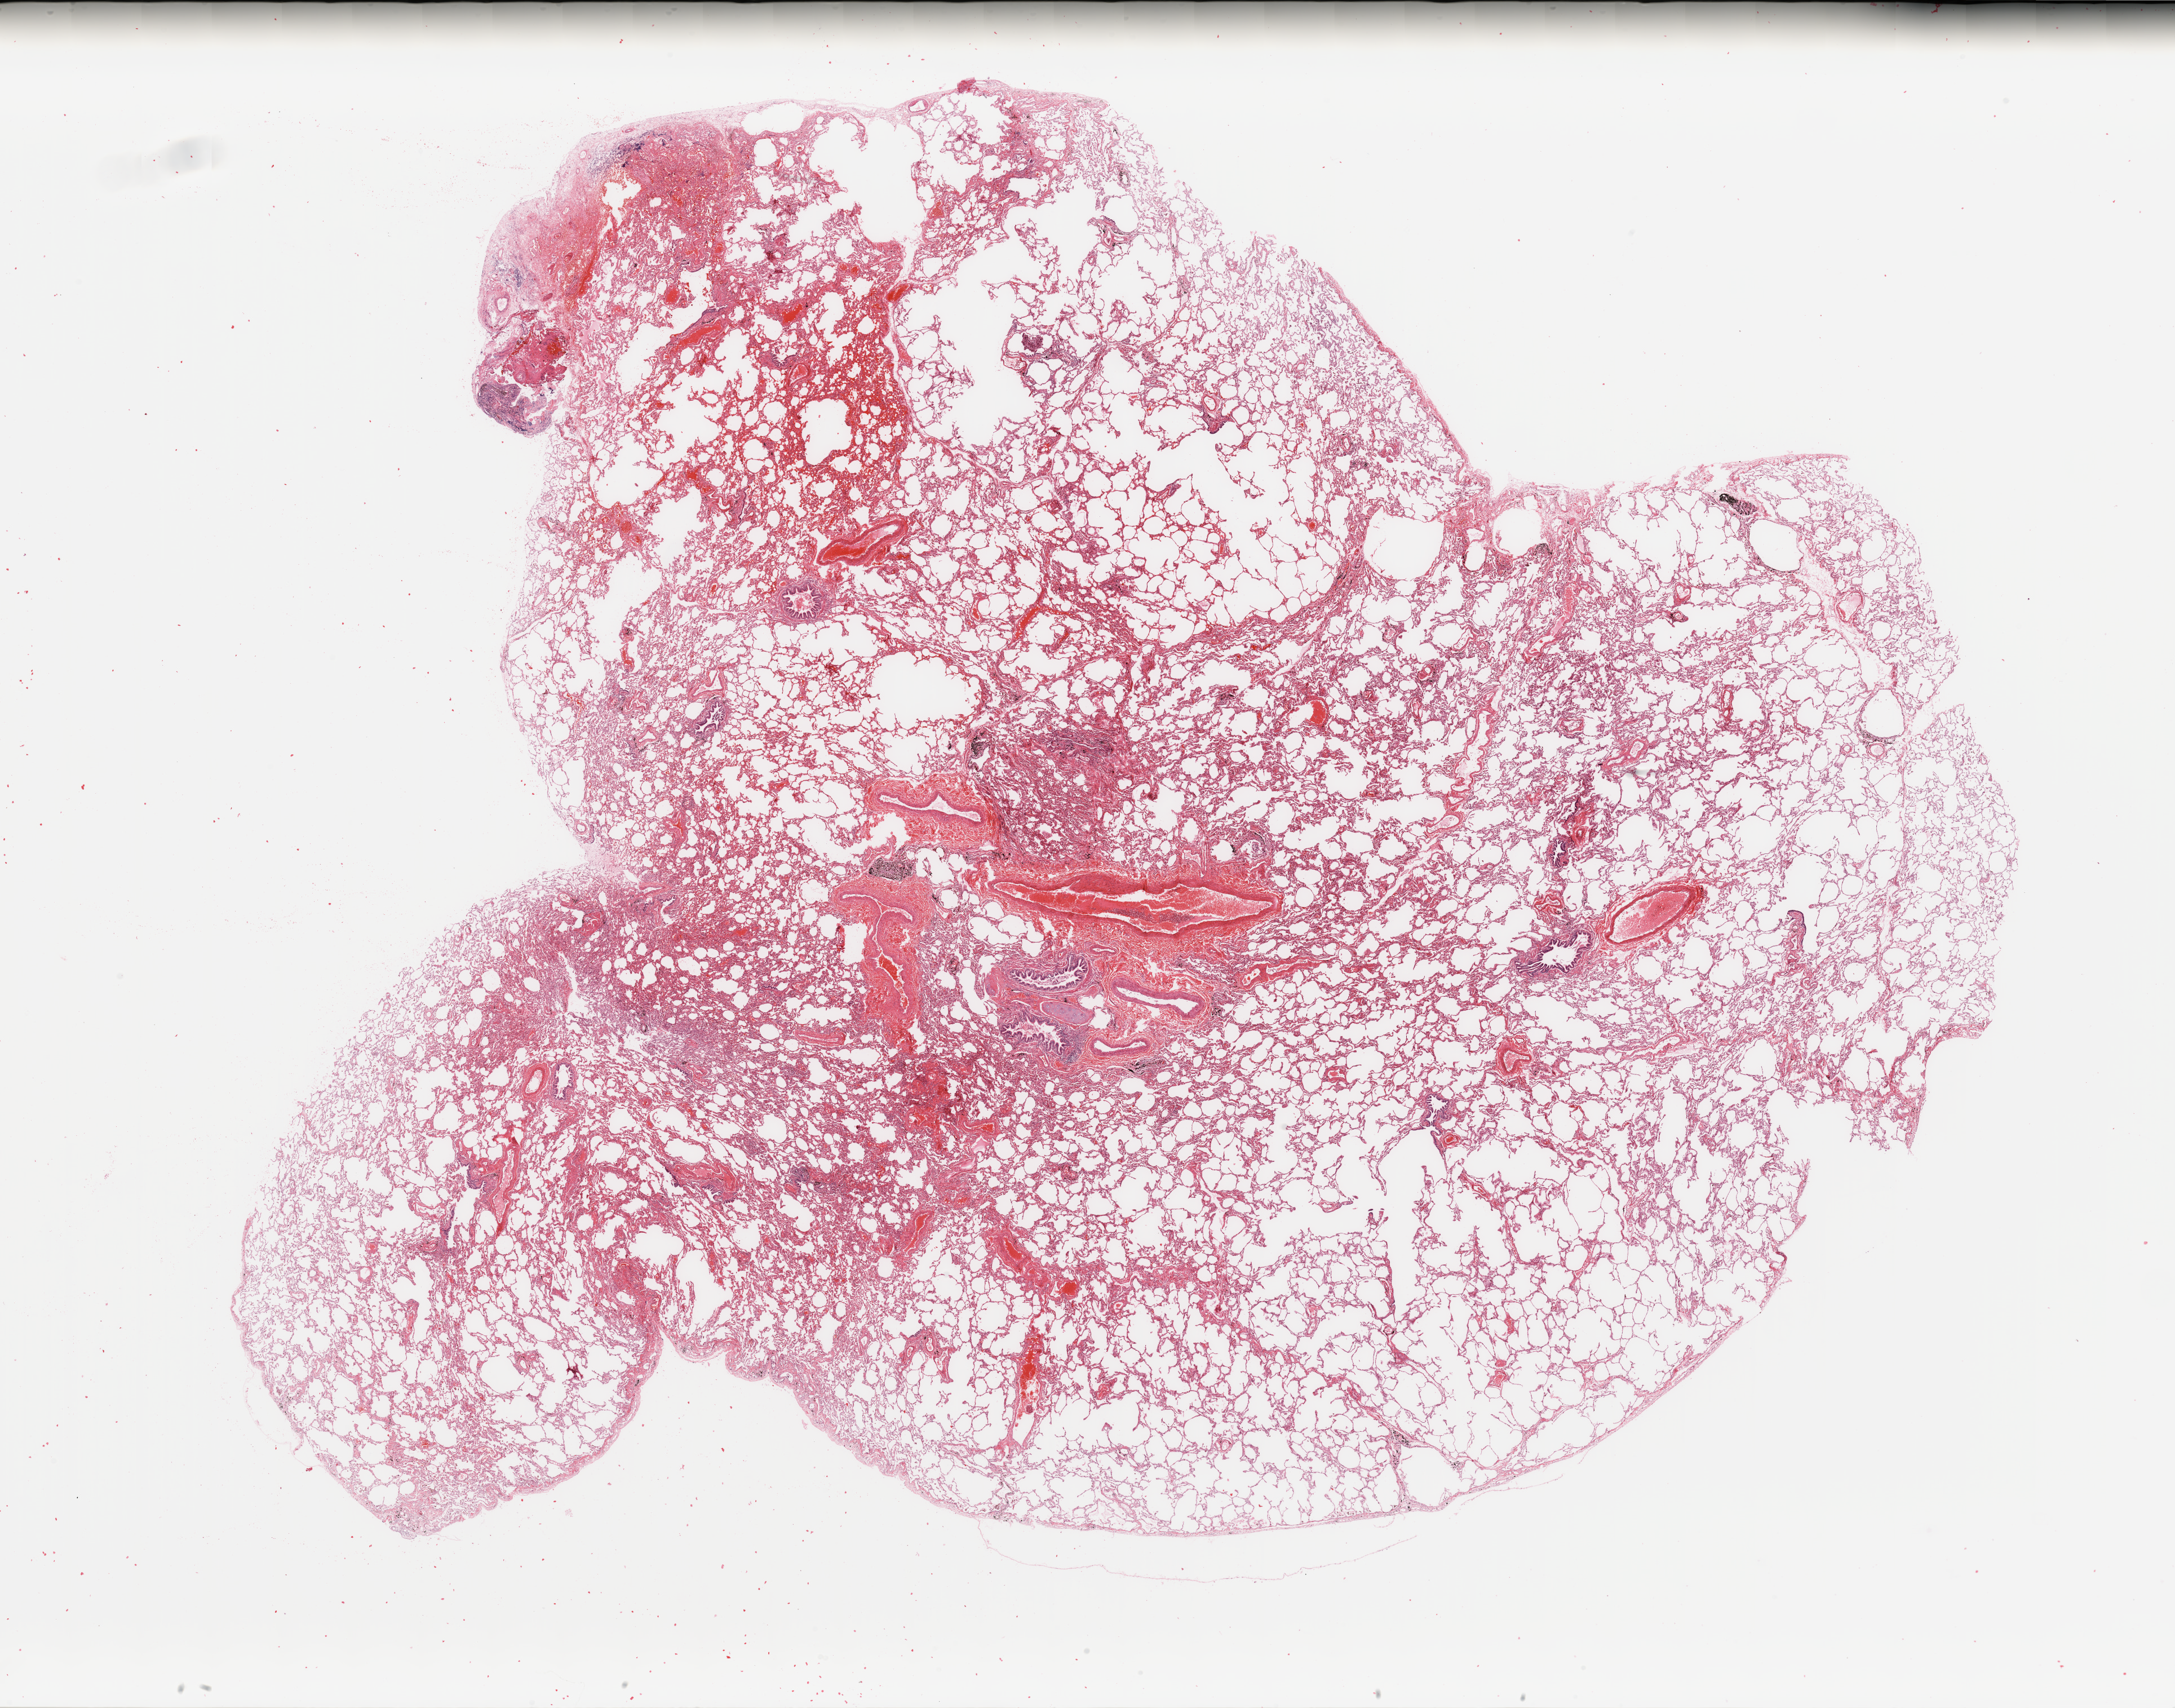
Whole-slide histology image, H&E-stained — shown as a low-resolution overview of the whole scanned area (about 30.5 x 24.0 mm), normal (non-tumour) tissue sample, lung. Patient: male, age 45 years.
* this section: normal (non-tumour) tissue from the same patient
* patient diagnosis: Adenocarcinoma, NOS